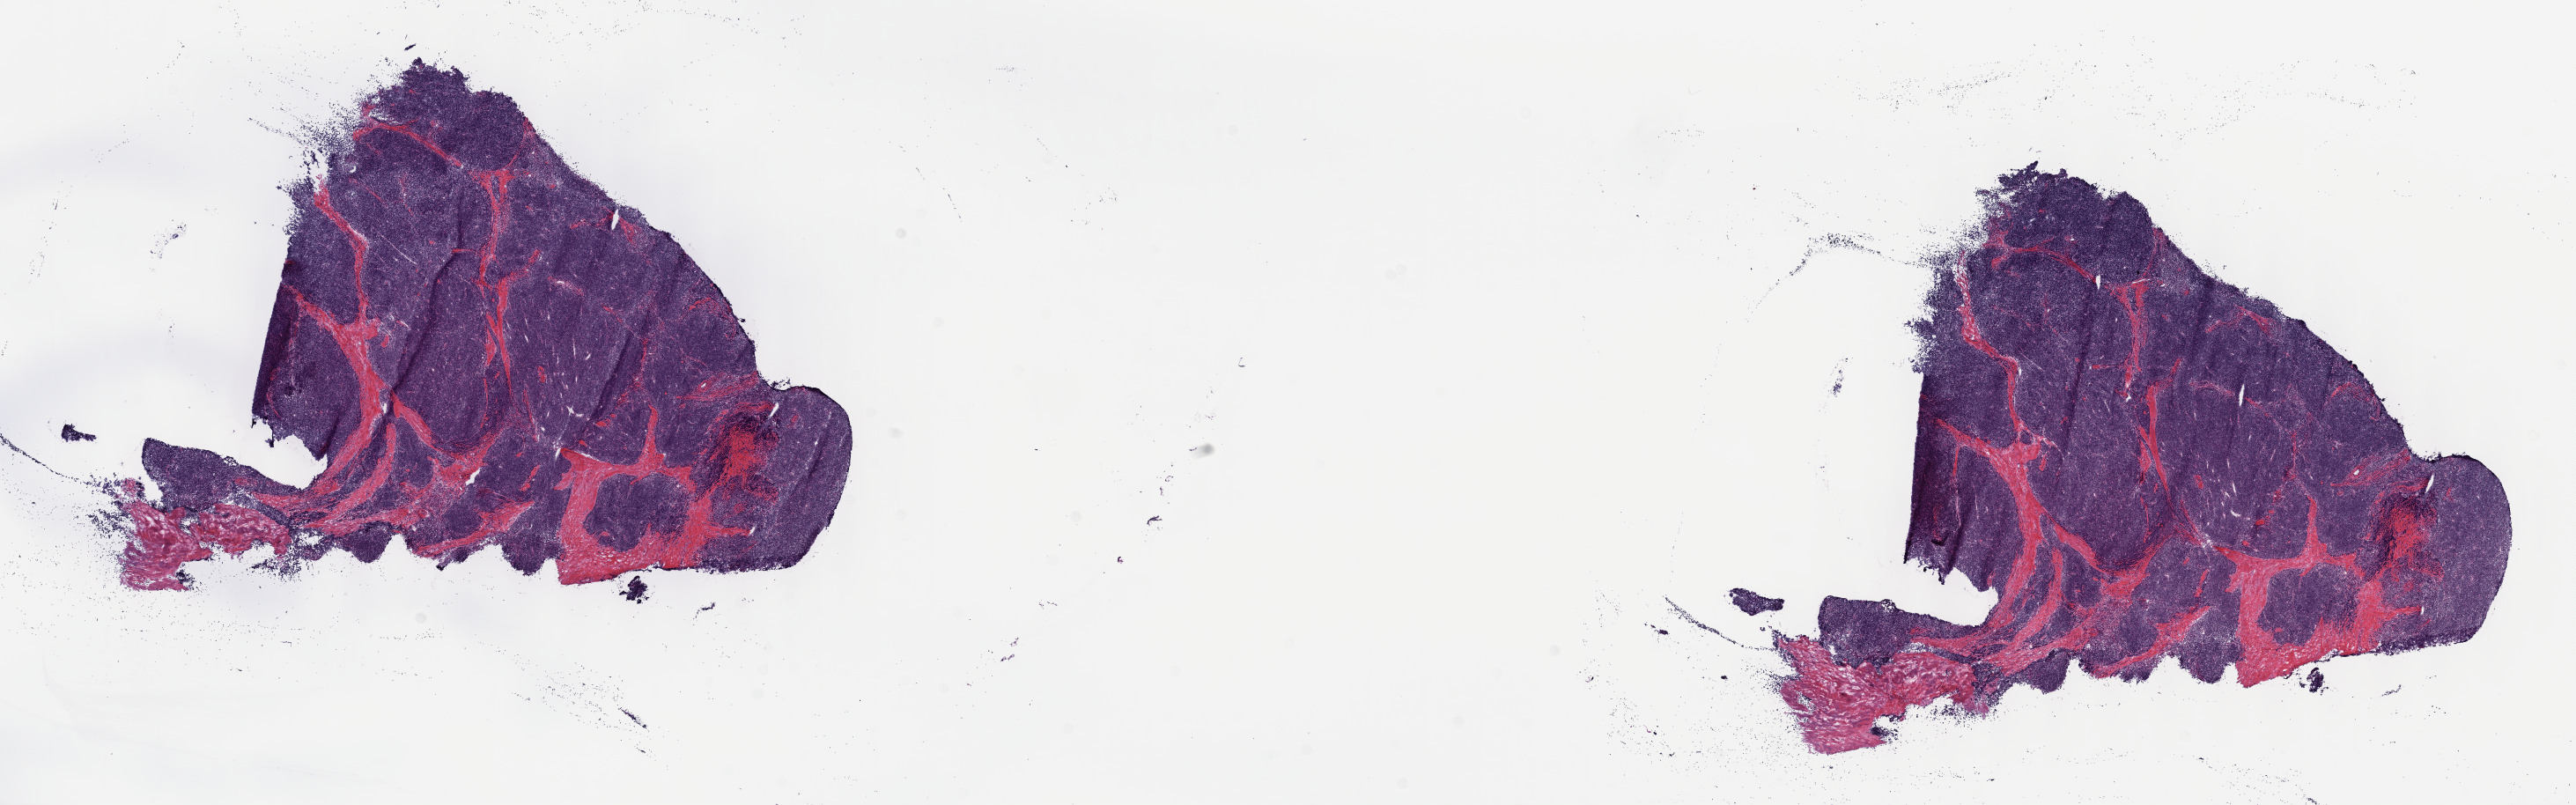
Whole-slide histology image, H&E-stained, low-resolution overview of the scanned area, about 23.7 x 7.4 mm; frozen section; primary tumour sample from the thymus. Female, age 54 years at initial diagnosis. Slide review estimates, as recorded: tumour cells 100%, tumour nuclei 75%, normal cells 0%, stromal cells 0%, necrosis 0%. Infiltration values recorded for this section: lymphocyte infiltration 2%, monocyte infiltration 0%, neutrophil infiltration 0%.
- pathologic diagnosis: Thymoma, type B1, malignant (anterior mediastinum)